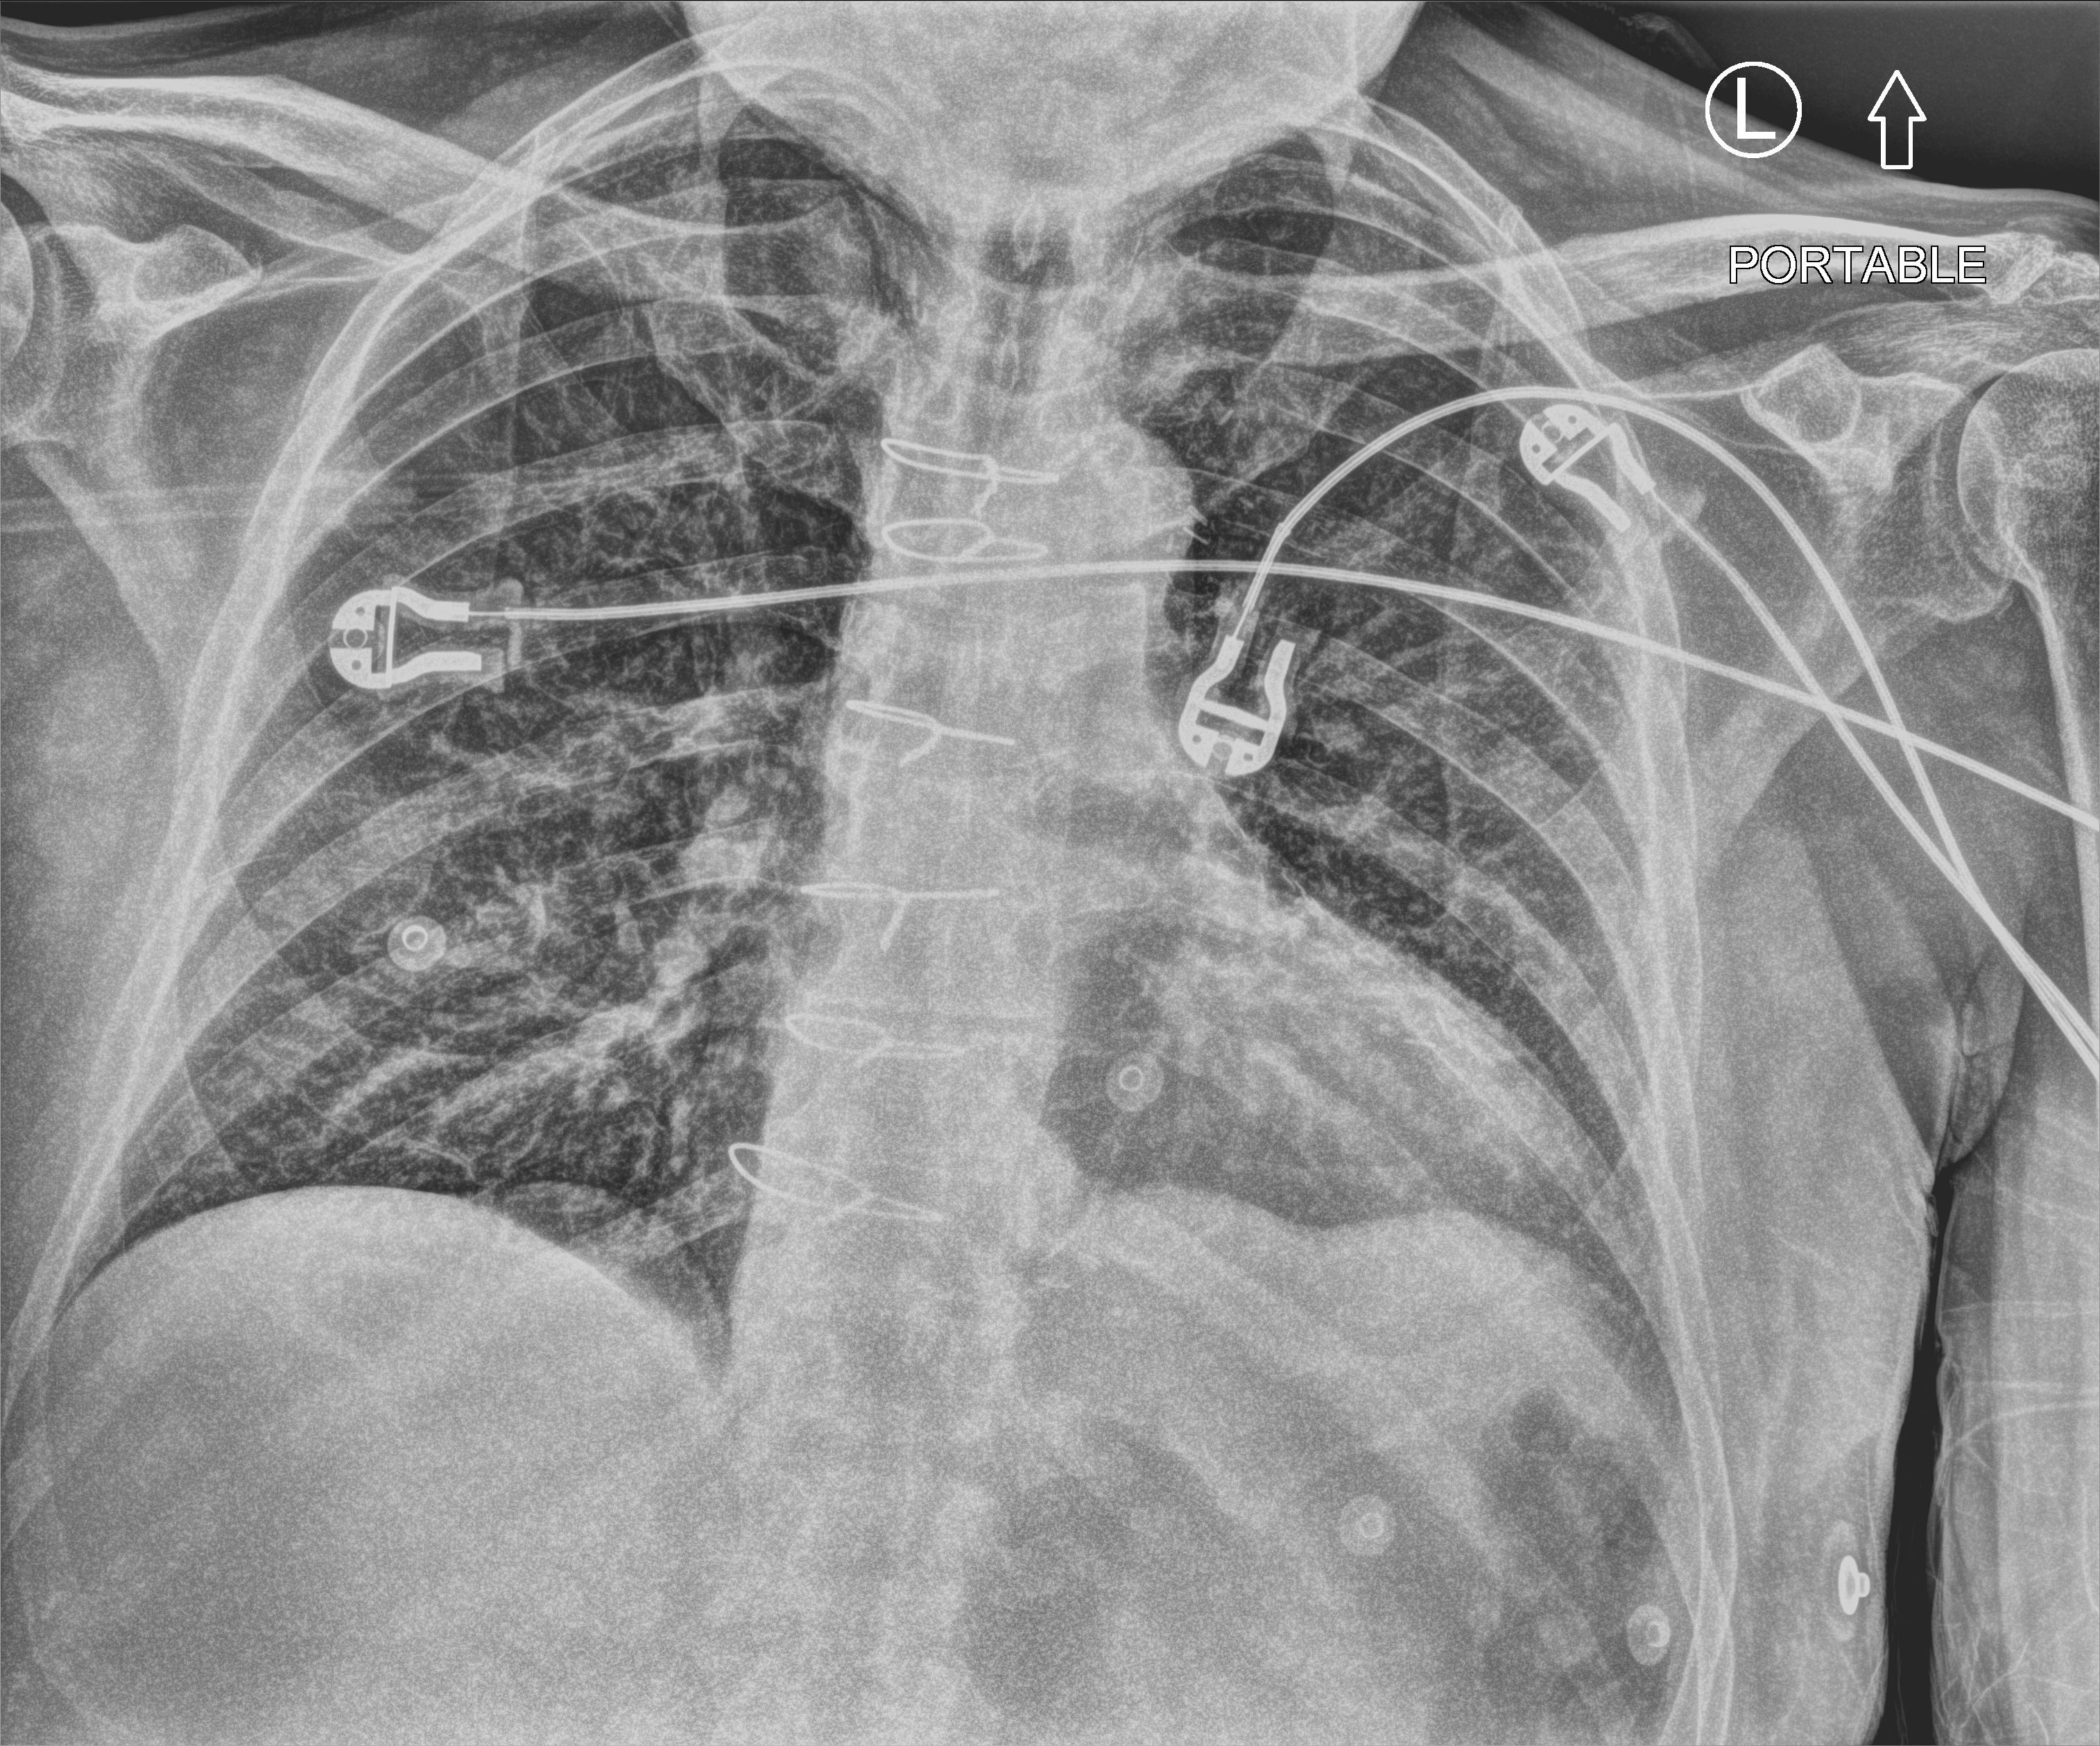
Chest X-ray (portable); anteroposterior (AP) projection. Male patient hospitalised with COVID-19, age 75–90 years.
From the hospital-stay record, not from the radiograph (when in the stay this image was taken is not recorded):
- COPD (admission record): yes